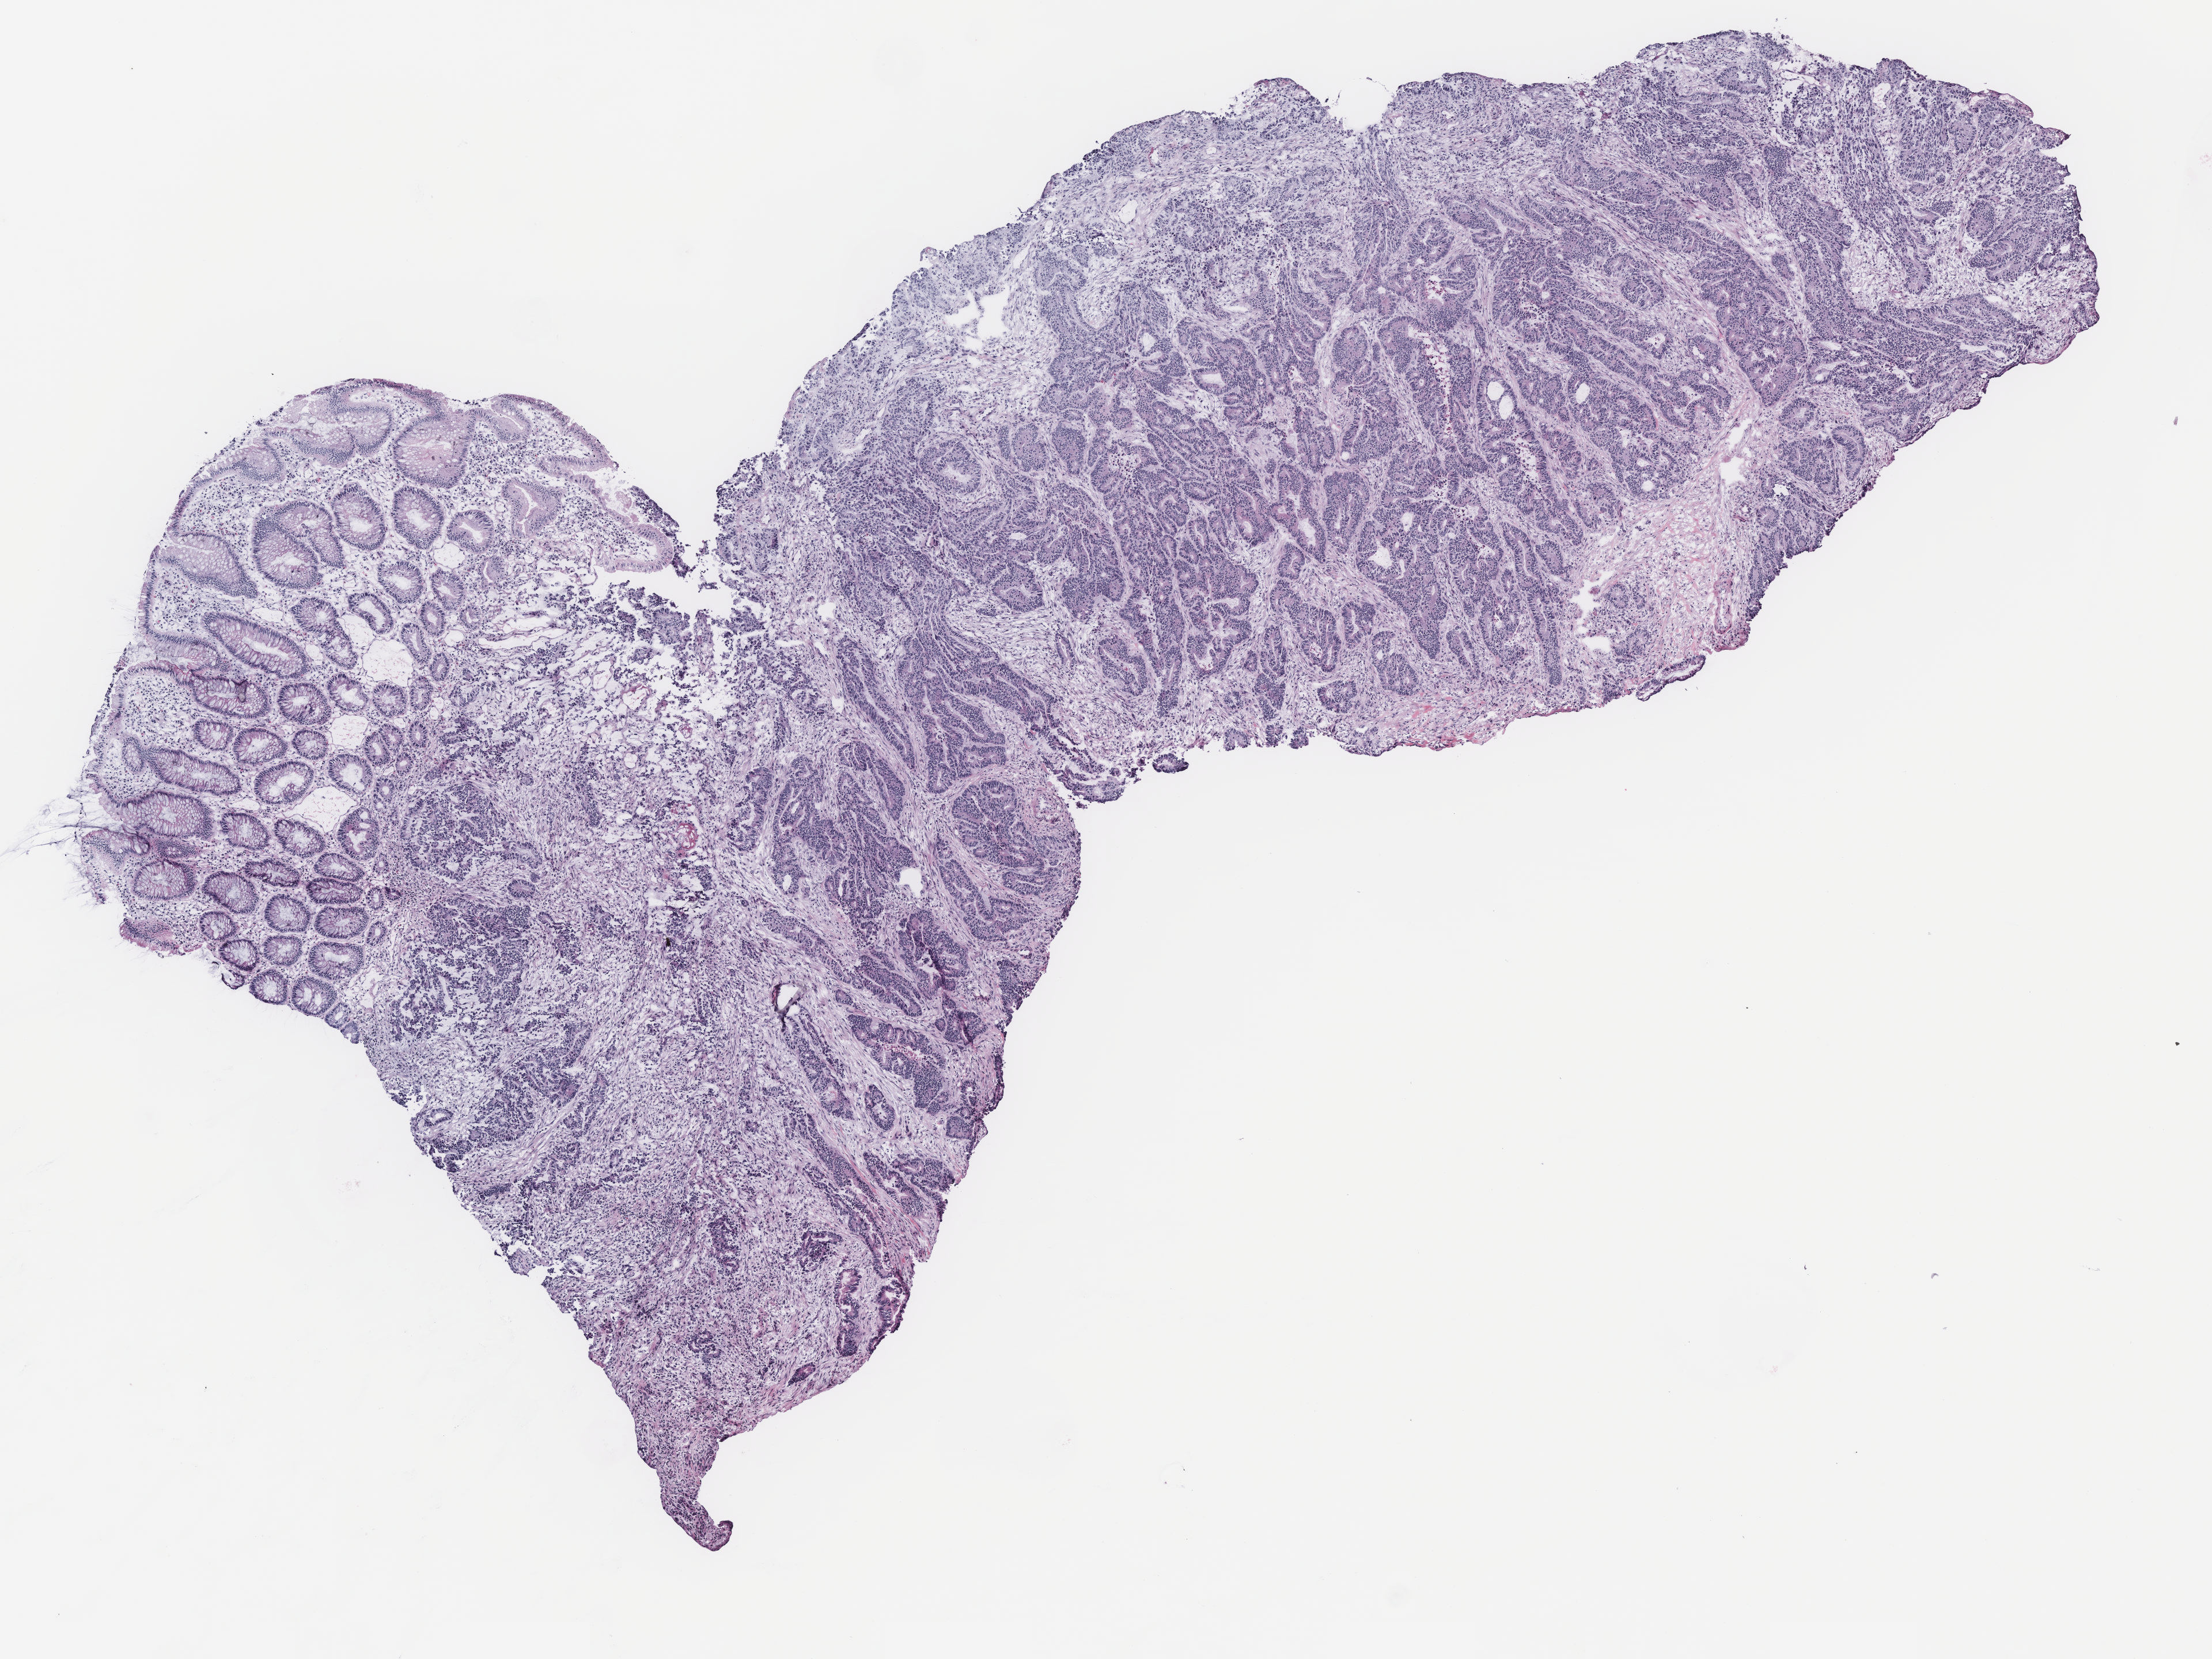
Hematoxylin and eosin (H&E) stained whole-slide image, low-resolution overview of the scanned area, about 7.7 x 5.8 mm, colon, tissue type not recorded.
Patient diagnosis (cohort enrolment): colon cancer (colon).